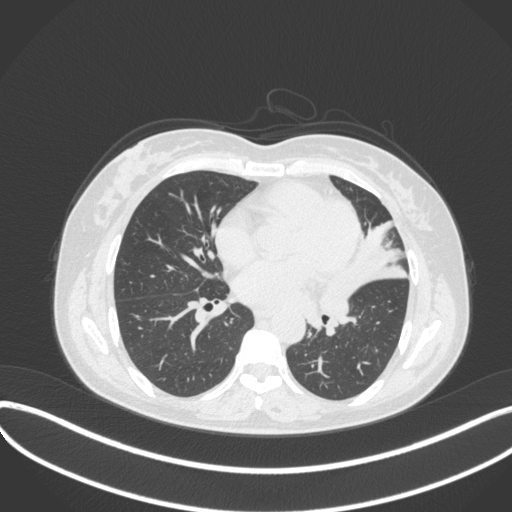
Chest CT, one axial slice; lung window (W 1500 / L -600 HU); 1 mm slice thickness; 512 × 512 image matrix, field of view 400 × 400 mm. Patient: female, 54 years. Case-level facts recorded for this patient, not image findings: clinical TNM (as recorded): T2a N1 M0.
Annotated regions visible in this slice (bounding box drawn by a radiologist):
- lung tumour (recorded histology: small cell carcinoma): box from (x=319, y=271) to (x=362, y=328) px